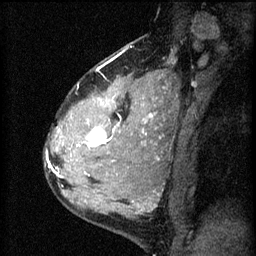
Breast MRI (dynamic contrast-enhanced), one sagittal slice; slice 42 of 60 in the series (ordered by position); 3 images stored at this slice position (order not interpretable as contrast timing); 1.5 T; TE 4.2 ms, TR 8.2 ms; 2 mm slice thickness; 256 × 256 image matrix, field of view 180 × 180 mm. Female patient, age 37 years.
Structures marked on this image (semi-automatically segmented with operator editing):
- analysis volume of interest (the breast-tissue region the enhancement analysis was run in; not a lesion): box from (x=53, y=78) to (x=140, y=181) px
- tumour enhancement mask (voxels above the 70 % enhancement threshold inside the analysis volume of interest): (x=56, y=122)–(x=120, y=177)